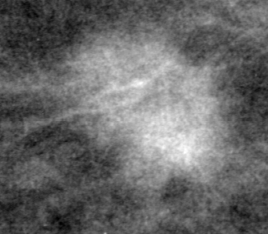
Region of interest cut from a scanned film mammogram (one marked finding), left breast, CC view, BI-RADS breast density category 2 (scale 1–4).
- Mass, shape oval, margins ill defined; BI-RADS assessment category 5; pathology result (as recorded, not read from the image): malignant.